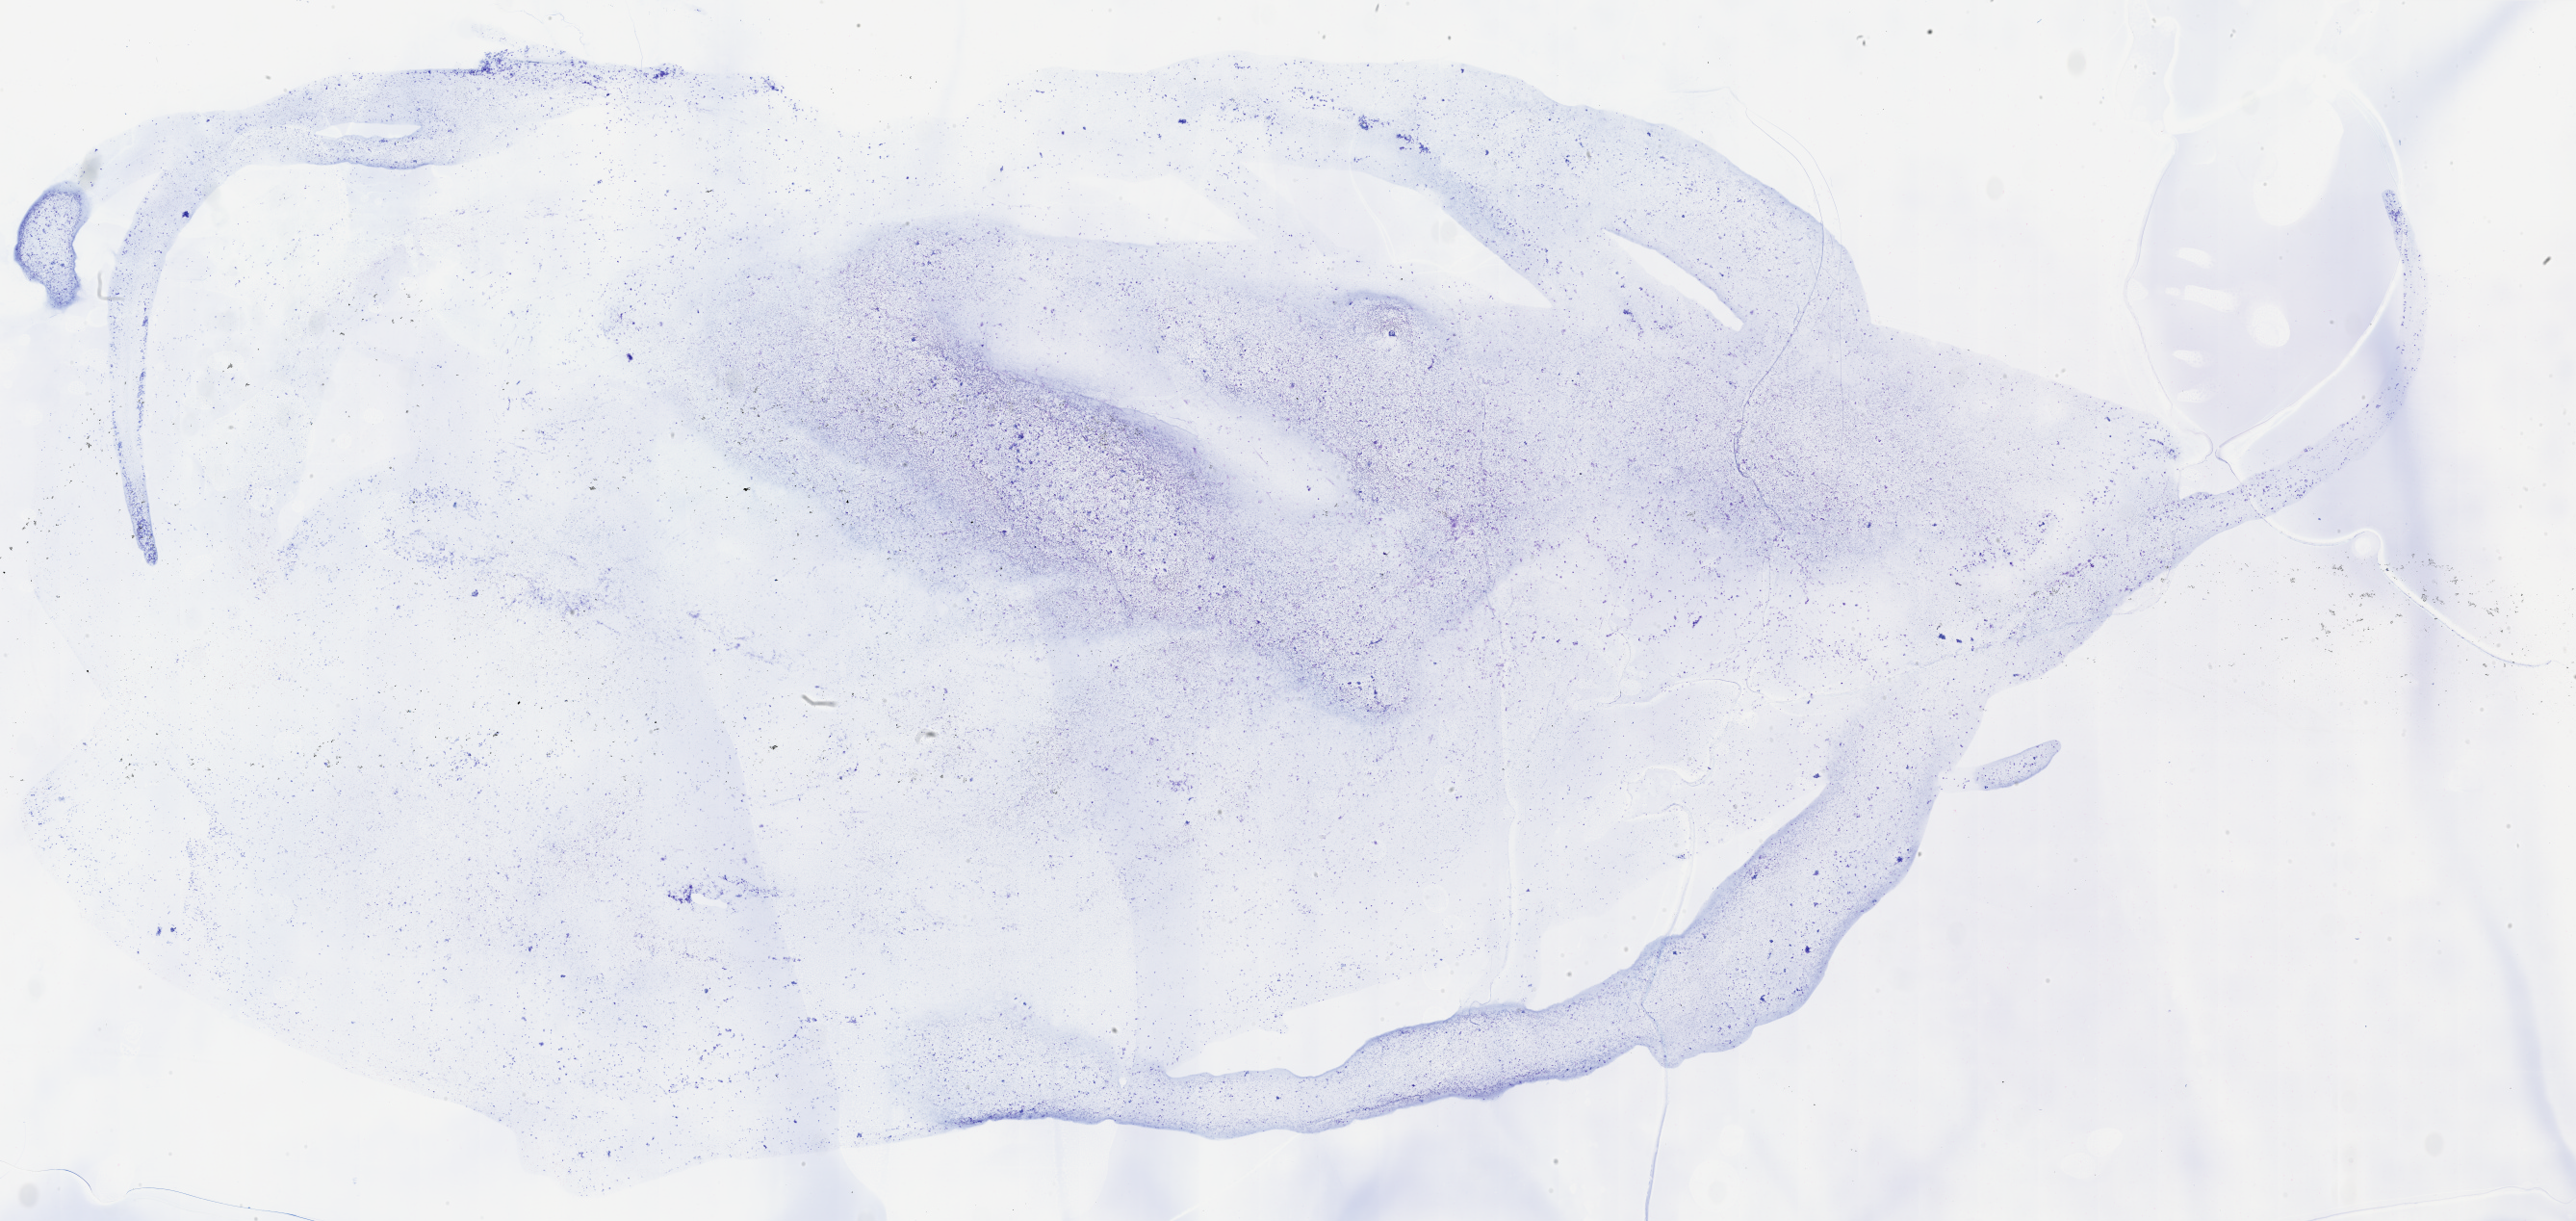
Digitized hematoxylin and eosin (H&E)-stained section of the patient's (originator) tumor tissue — whole scanned area (about 42.9 x 20.3 mm) shown as a low-resolution overview. Formalin-fixed paraffin-embedded section. Originating tumor site category: colon. Female patient.
Diagnosis: Colon Adenocarcinoma.